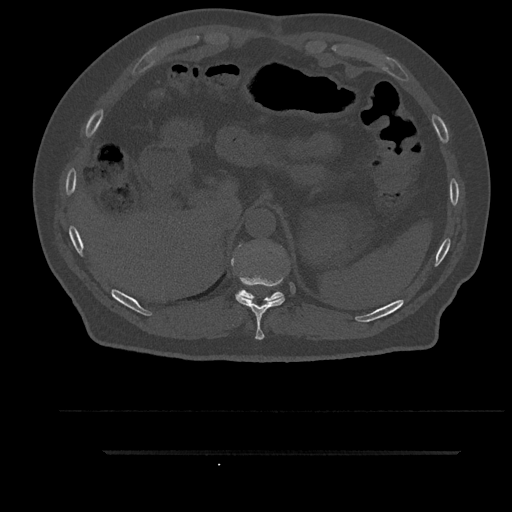
CT including the spine, one axial slice; slice 340 of 797 in the series (ordered by position); bone window (W 1800 / L 400 HU); 0.5 mm slice thickness; 512 × 512 image matrix, field of view 432 × 432 mm. Patient: male, 63 years. From the clinical record (not read from this slice): primary cancer: renal.
Outlined on this slice (semi-automatic segmentation, software-assisted and operator-edited):
- T10 vertebra: bounding box <231,245,285,340> (left, top, right, bottom; pixels)
- T11 vertebra: <236,290,284,302>